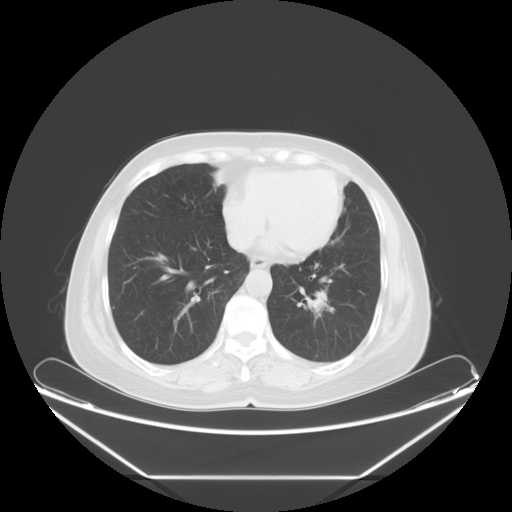
Chest CT, one axial slice. Position 22 of 61 along the scan axis. Lung window (W 1500 / L -600 HU). 5 mm slice thickness. 512 × 512 image matrix. Female patient, age 63 years. From the clinical record (not read from this slice): clinical TNM (as recorded): T1c N0 M0; histopathological grade: G2-3.
Structures marked on this image (bounding box drawn by a radiologist):
- lung tumour (recorded histology: adenocarcinoma): bounding box [x1, y1, x2, y2] px = [303, 283, 335, 319]